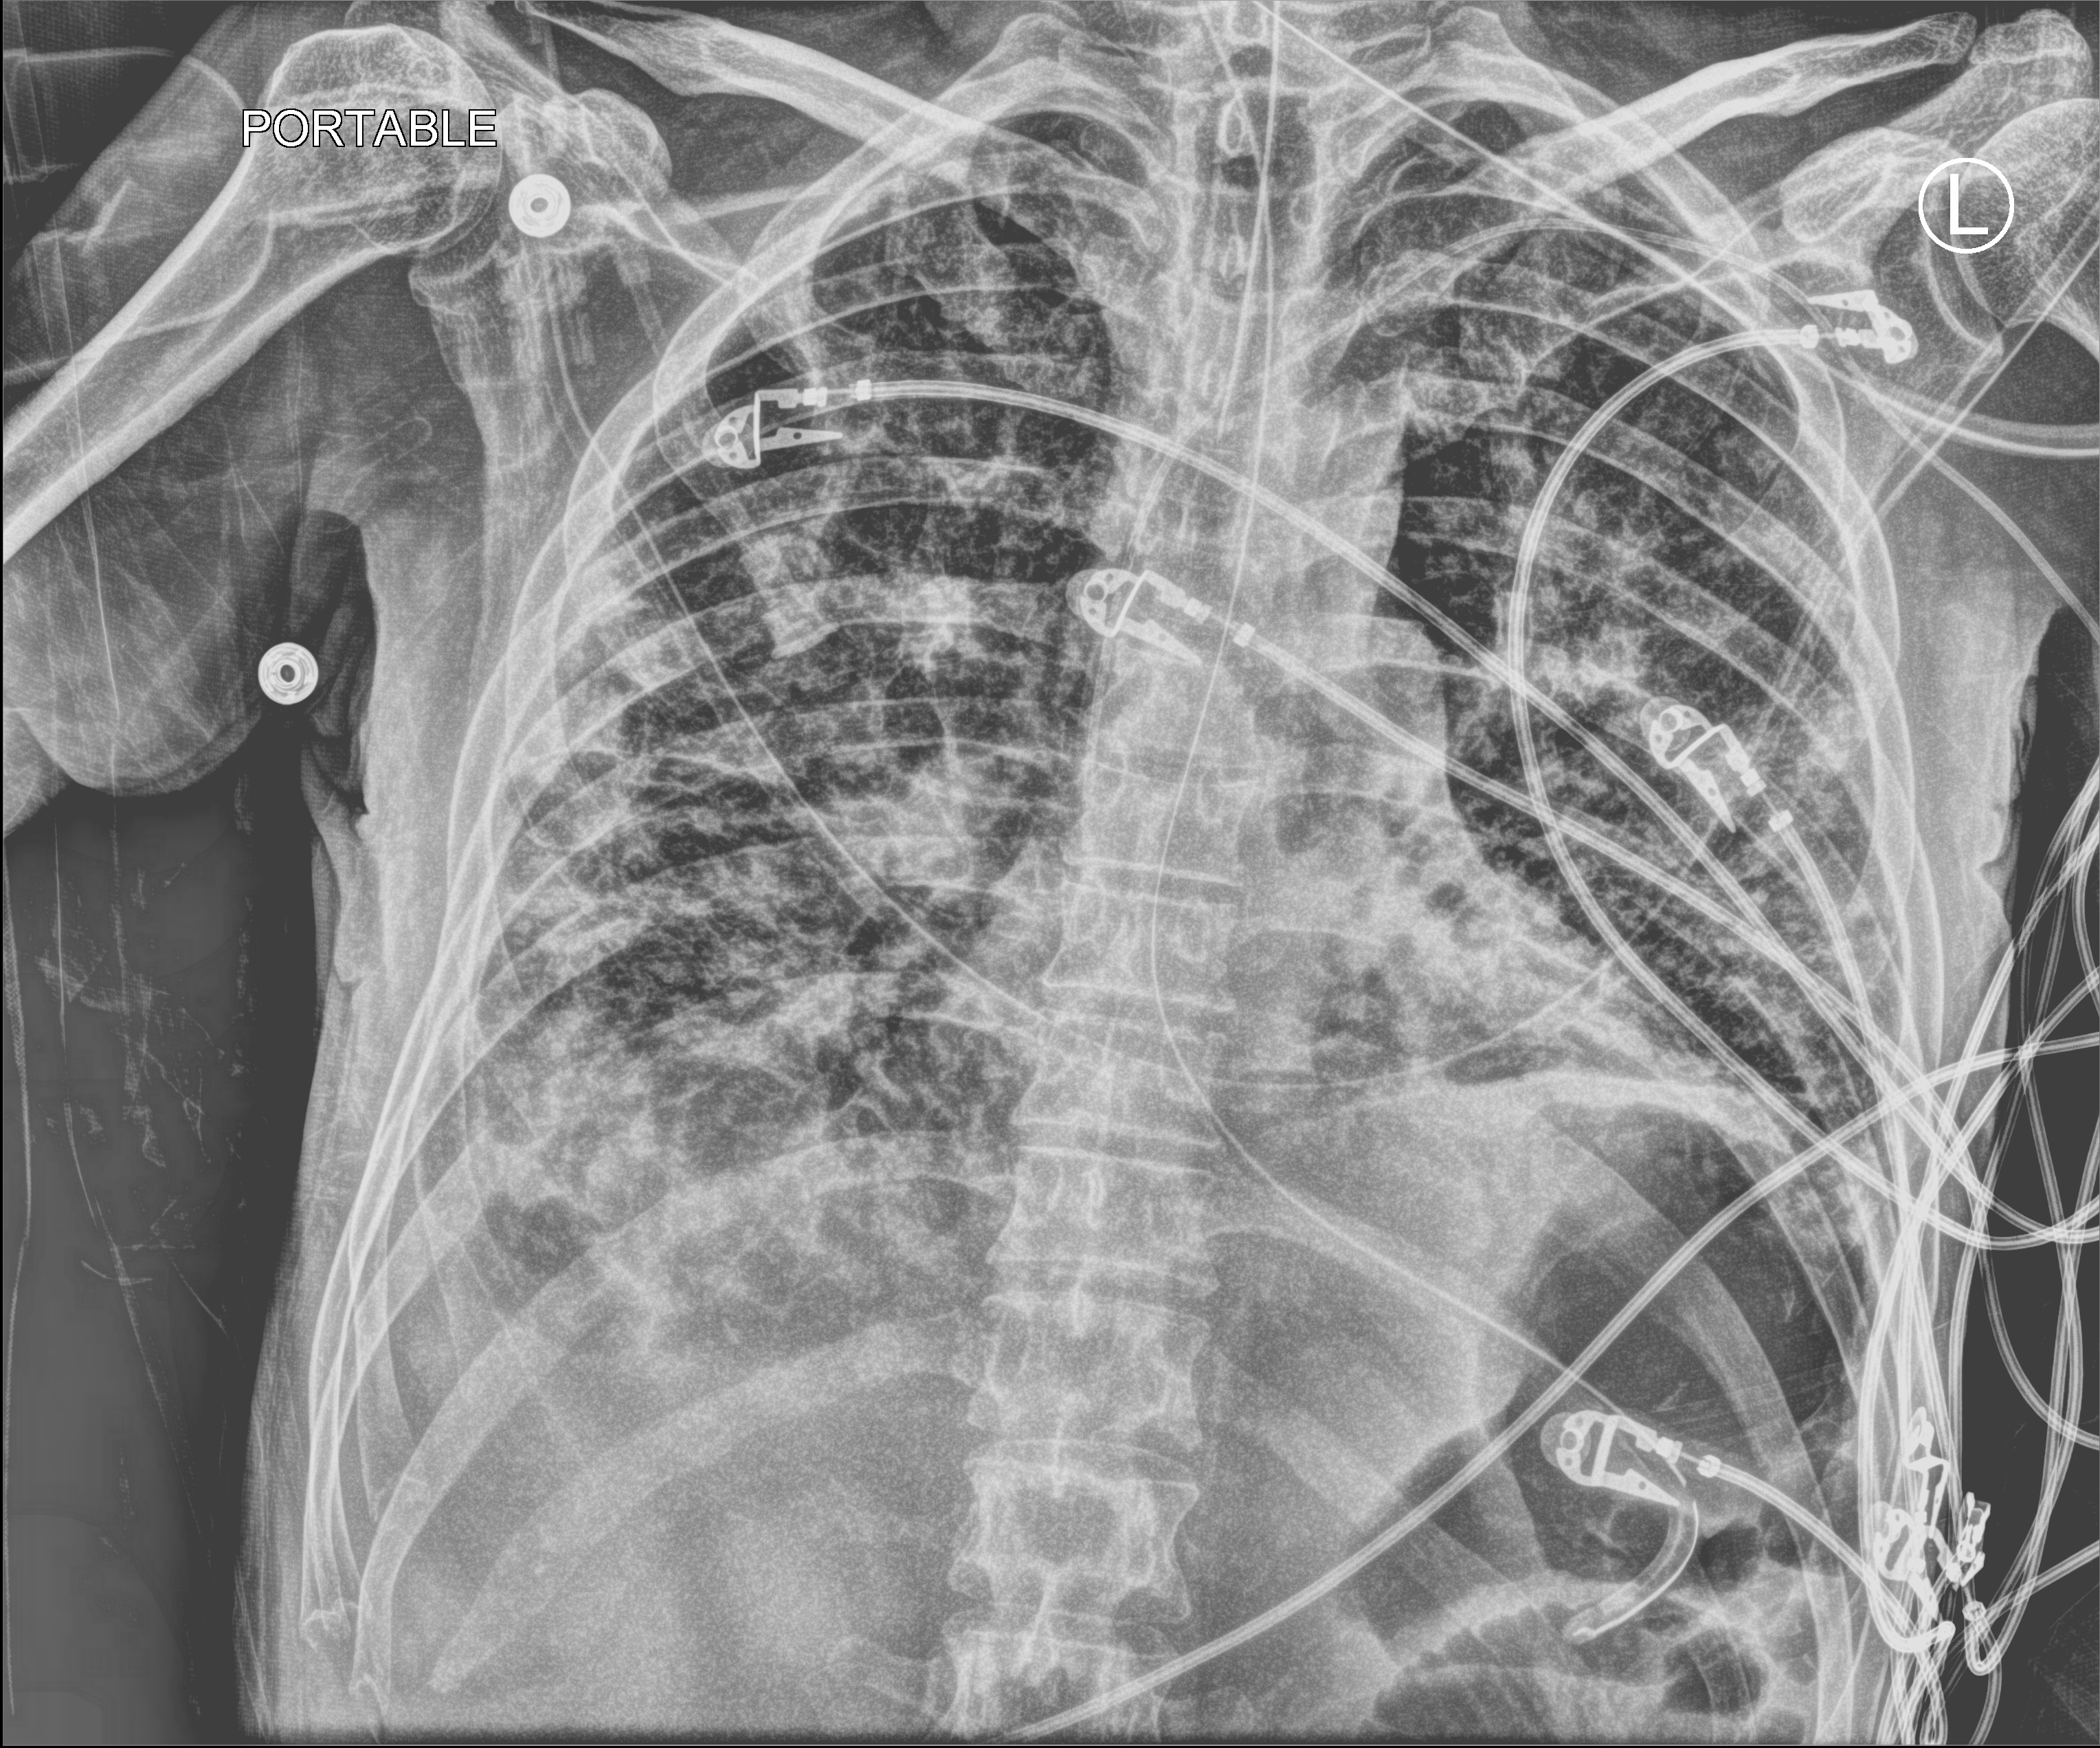
Chest X-ray (portable), anteroposterior (AP) projection. Patient hospitalised with COVID-19; male, aged 18–59 years.
From the hospital-stay record, not from the radiograph (when in the stay this image was taken is not recorded): hypertension (admission record): yes.